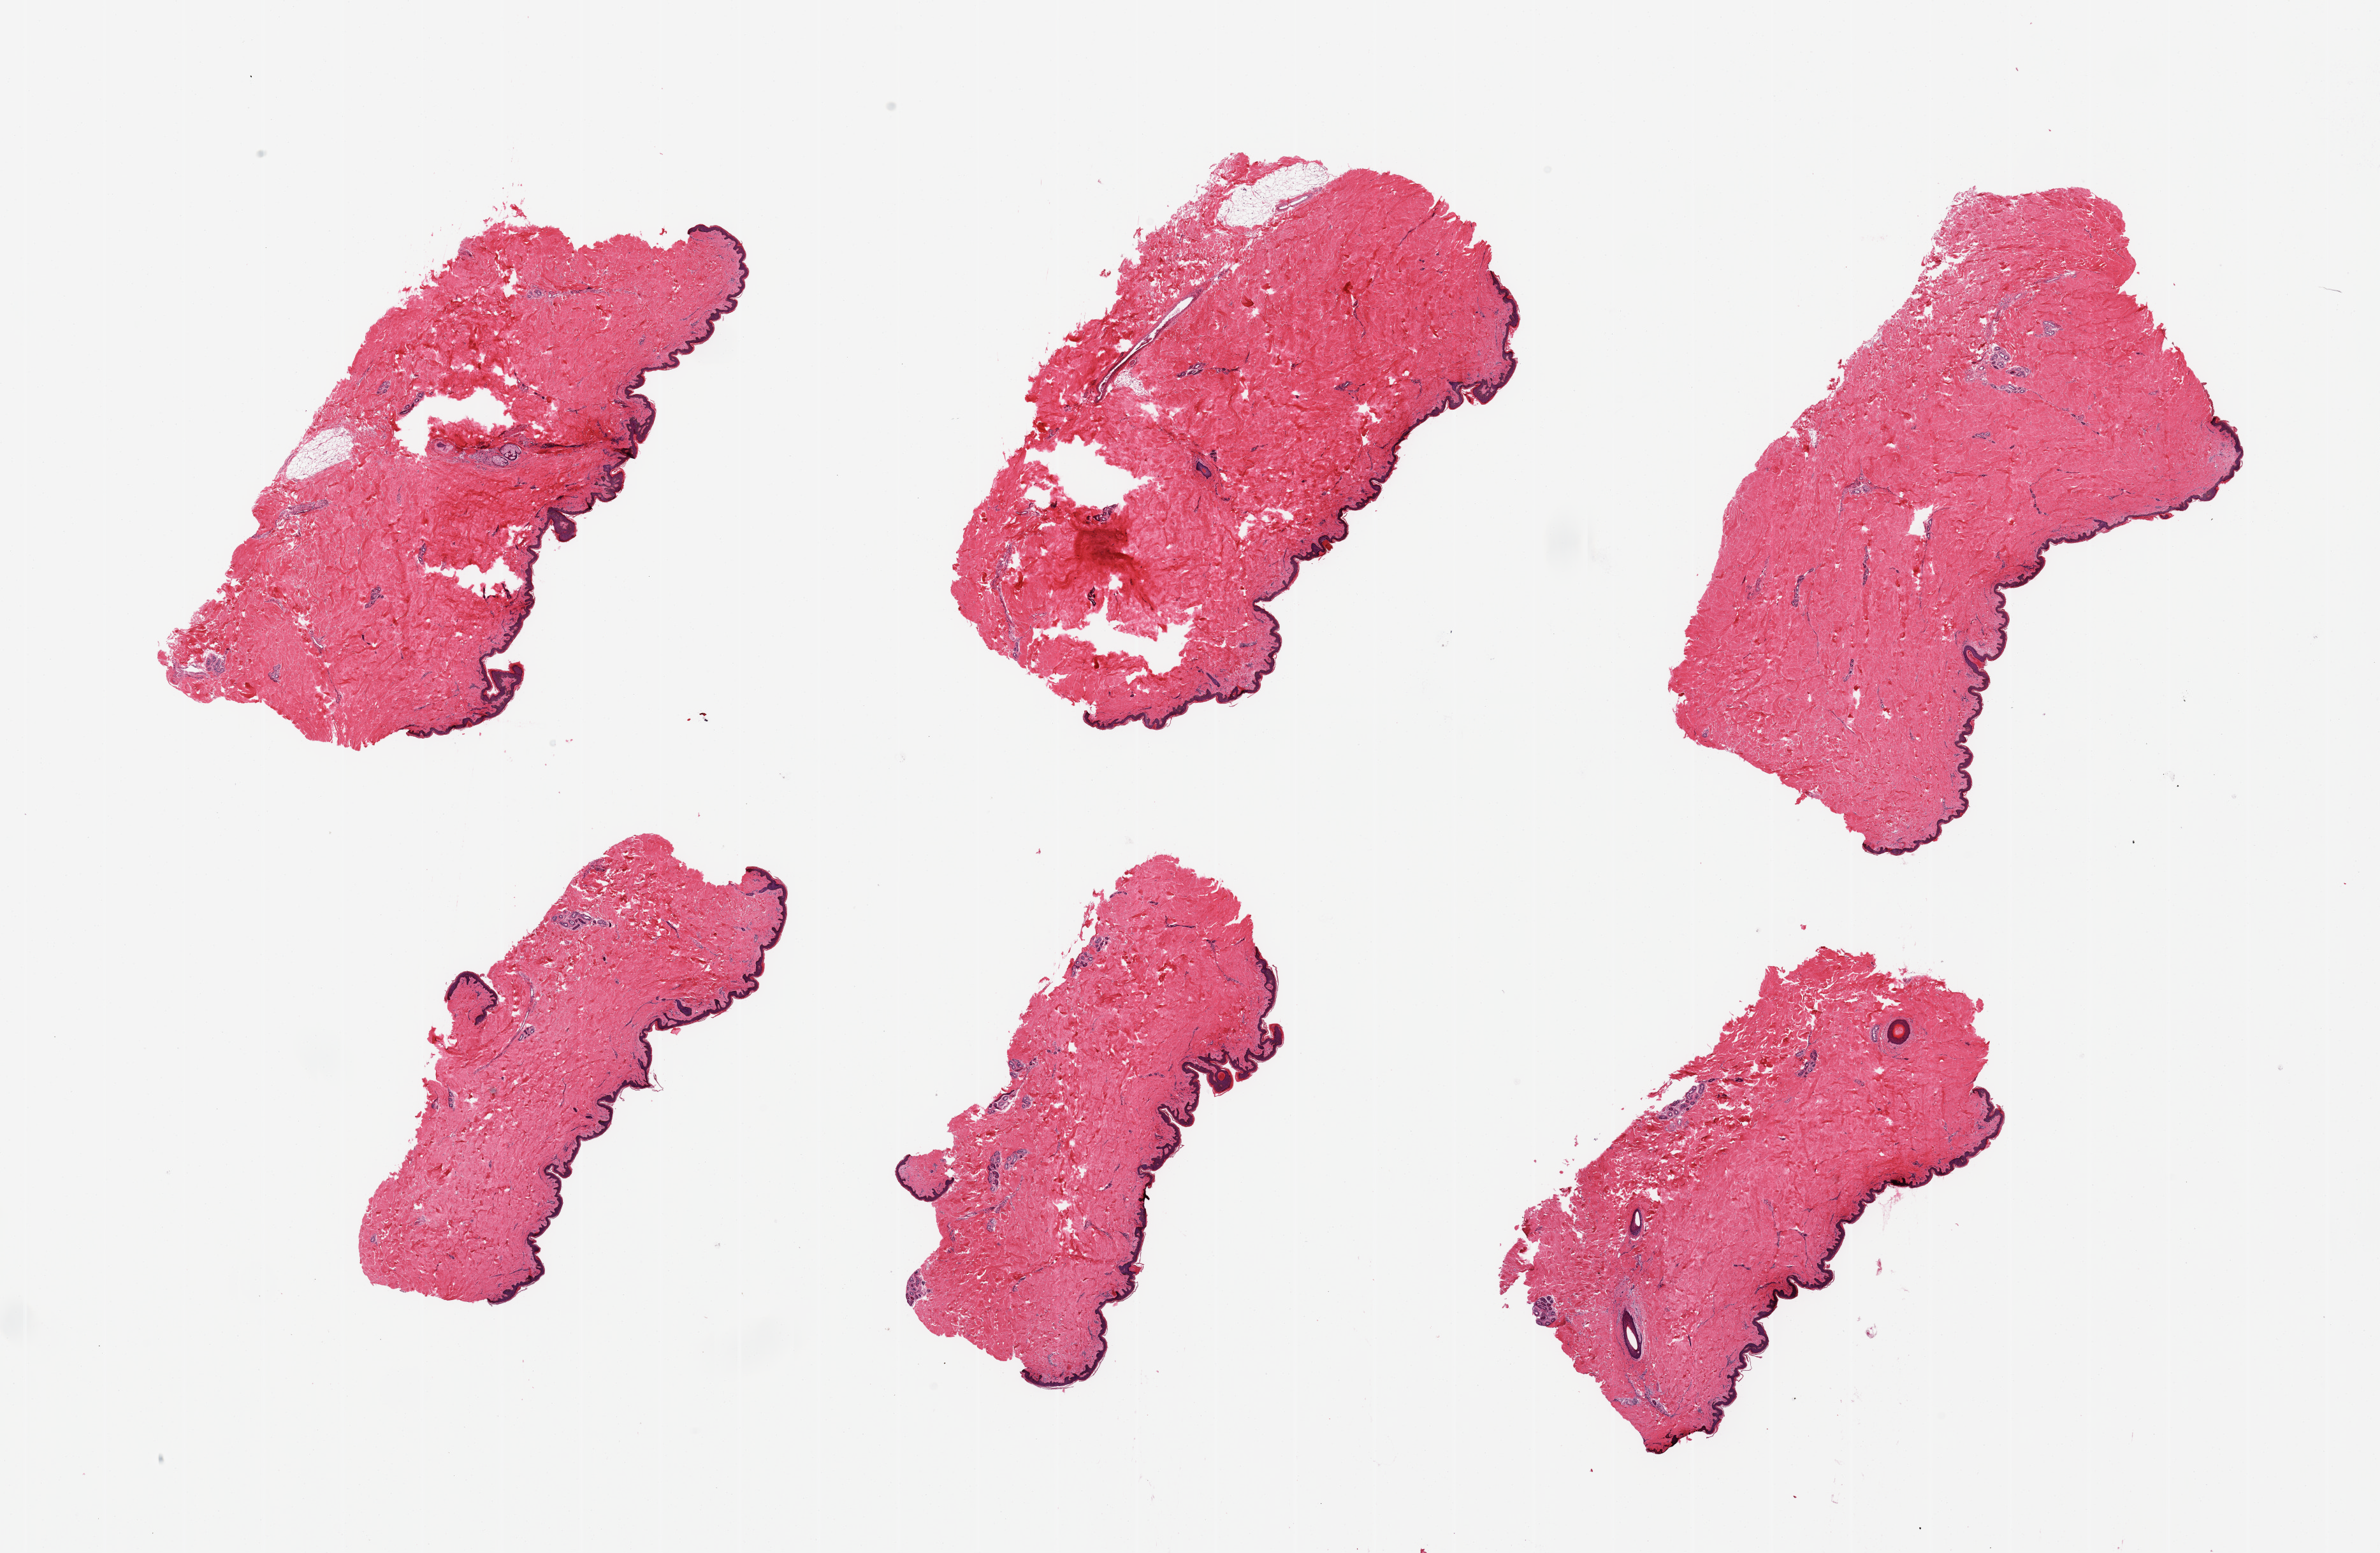
H&E whole-slide image — shown as a low-resolution overview of the whole scanned area (about 29.5 x 19.3 mm); PAXgene-fixed, paraffin-embedded tissue; sampled site (target tissue): skin of suprapubic region; tissue donor sample. Donor sex: male.
Review note (as recorded): 6 pieces; well trimmed; <1% dermal fat.